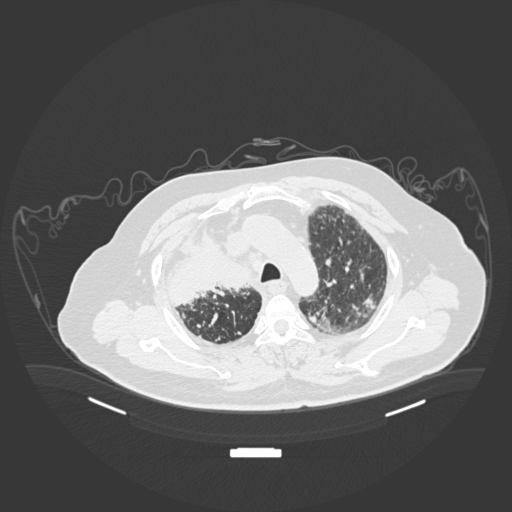
Chest CT, one axial slice; reconstruction kernel B30f; 120 kVp; lung window (W 1500 / L -600 HU); 1 mm slice thickness; 512 × 512 image matrix, field of view 500 × 500 mm. Male patient, age 69 years. From the clinical record (not read from this slice): clinical TNM (as recorded): T4 N3 M1.
Outlined on this slice (rectangle marked by the reading radiologist):
- lung tumour (recorded histology: adenocarcinoma): bounding box <167,226,256,308> (left, top, right, bottom; pixels)